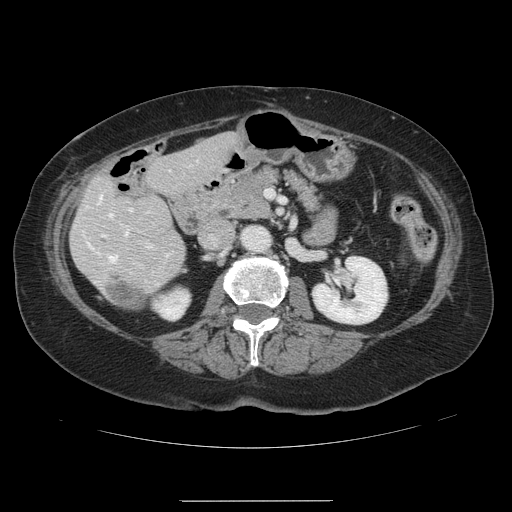
Contrast-enhanced abdominal CT, one axial slice. Position 50 of 141 along the scan axis. 120 kVp. Intravenous contrast given. Soft-tissue window (W 400 / L 40 HU). 2.5 mm slice thickness. 512 × 512 image matrix. Female patient, age 74 years. From the clinical record (not read from this slice): diagnosis: colorectal cancer liver metastases, imaged before liver resection; multiple liver metastases: yes; largest metastasis: 7 cm; disease in both lobes: yes.
Annotated regions visible in this slice (manually delineated by an expert):
- hepatic veins: bounding box (x1, y1, x2, y2) in pixels: (98, 196, 127, 262)
- liver: (71, 134, 238, 311)
- planned liver remnant (the part of the liver to remain after resection): (118, 134, 238, 256)
- portal vein (with intrahepatic branches): (102, 208, 152, 247)
- liver metastasis: (109, 283, 153, 307)